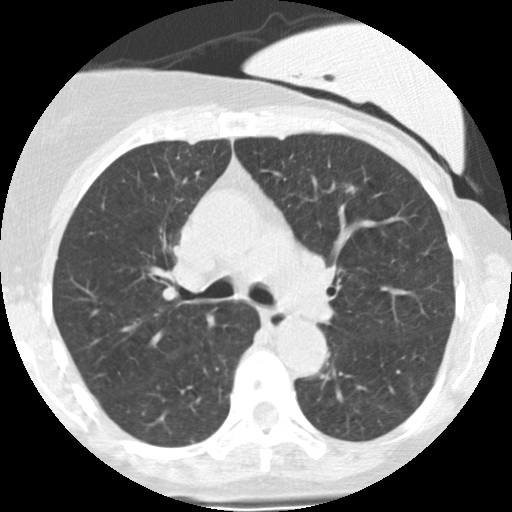
Low-dose screening chest CT, one axial slice. Position 160 of 251 along the scan axis. Reconstruction kernel STANDARD. Lung window (W 1500 / L -600 HU). 2.5 mm slice thickness. 512 × 512 image matrix, field of view 280 × 280 mm.
Outlined on this slice (manually delineated by an expert):
- lesion 1 (tumor, lower lobe of left lung): box from (x=346, y=185) to (x=355, y=194) px